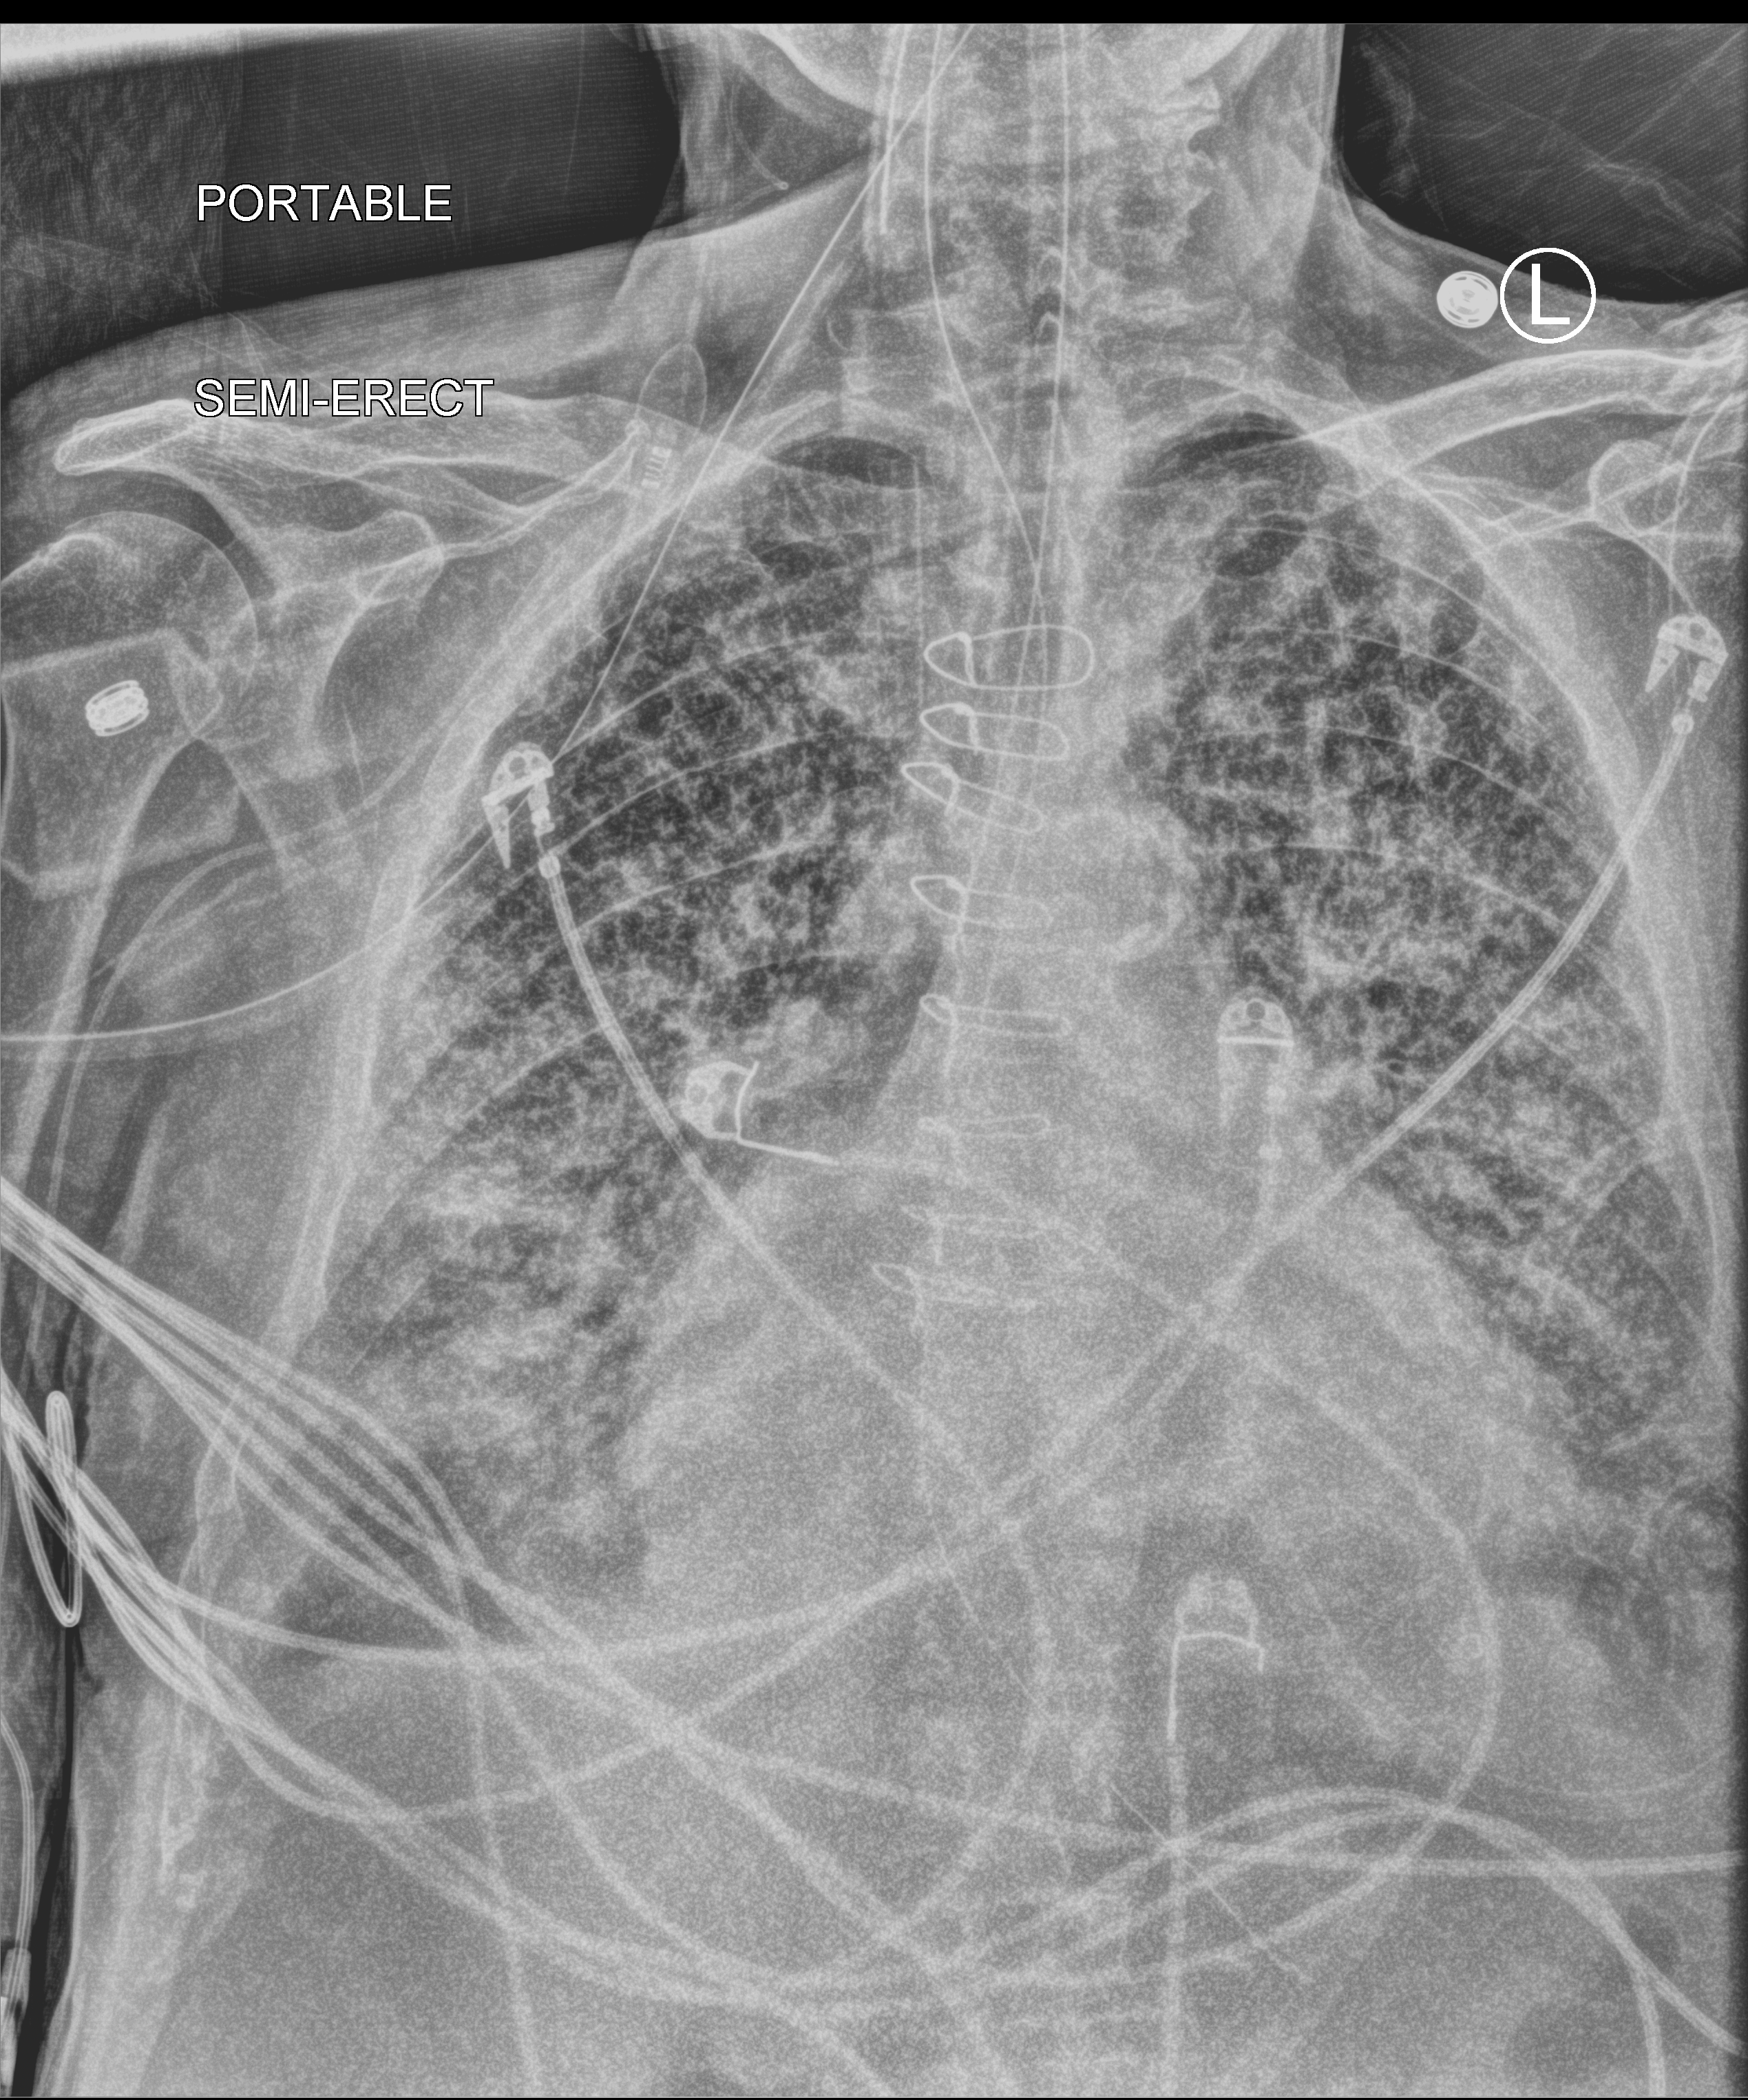
Portable chest radiograph; anteroposterior (AP) projection. Male patient hospitalised with COVID-19, age 75–90 years.
Admission-level facts for this patient (not findings on this image; timing relative to this image not recorded): length of hospital stay: 40 days.